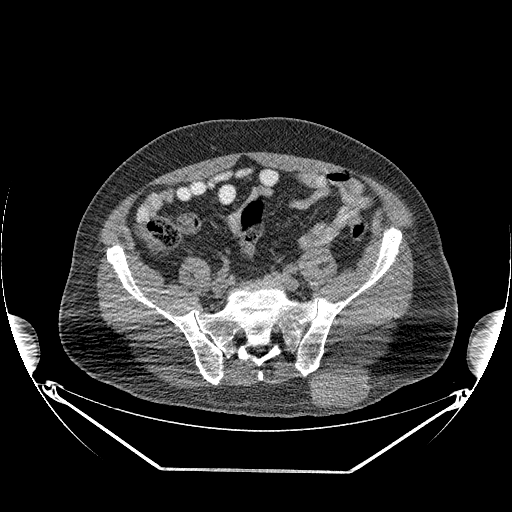
CT of an extremity soft-tissue mass (from a PET/CT study), one axial slice; slice 88 of 267 in the series (ordered by position); reconstruction kernel STANDARD; 140 kVp; soft-tissue window (W 400 / L 40 HU); 512 × 512 image matrix. Male patient. Case-level facts recorded for this patient, not image findings: histological type: pleiomorphic leiomyosarcoma; grade: high; site of the primary tumour: left buttock.
Annotated regions visible in this slice (expert contour drawn on MRI and transferred to this co-registered scan by the dataset authors):
- gross tumour volume including surrounding oedema: bounding box [x1, y1, x2, y2] px = [311, 368, 369, 407]
- gross tumour volume (mass): [311, 368, 368, 407]